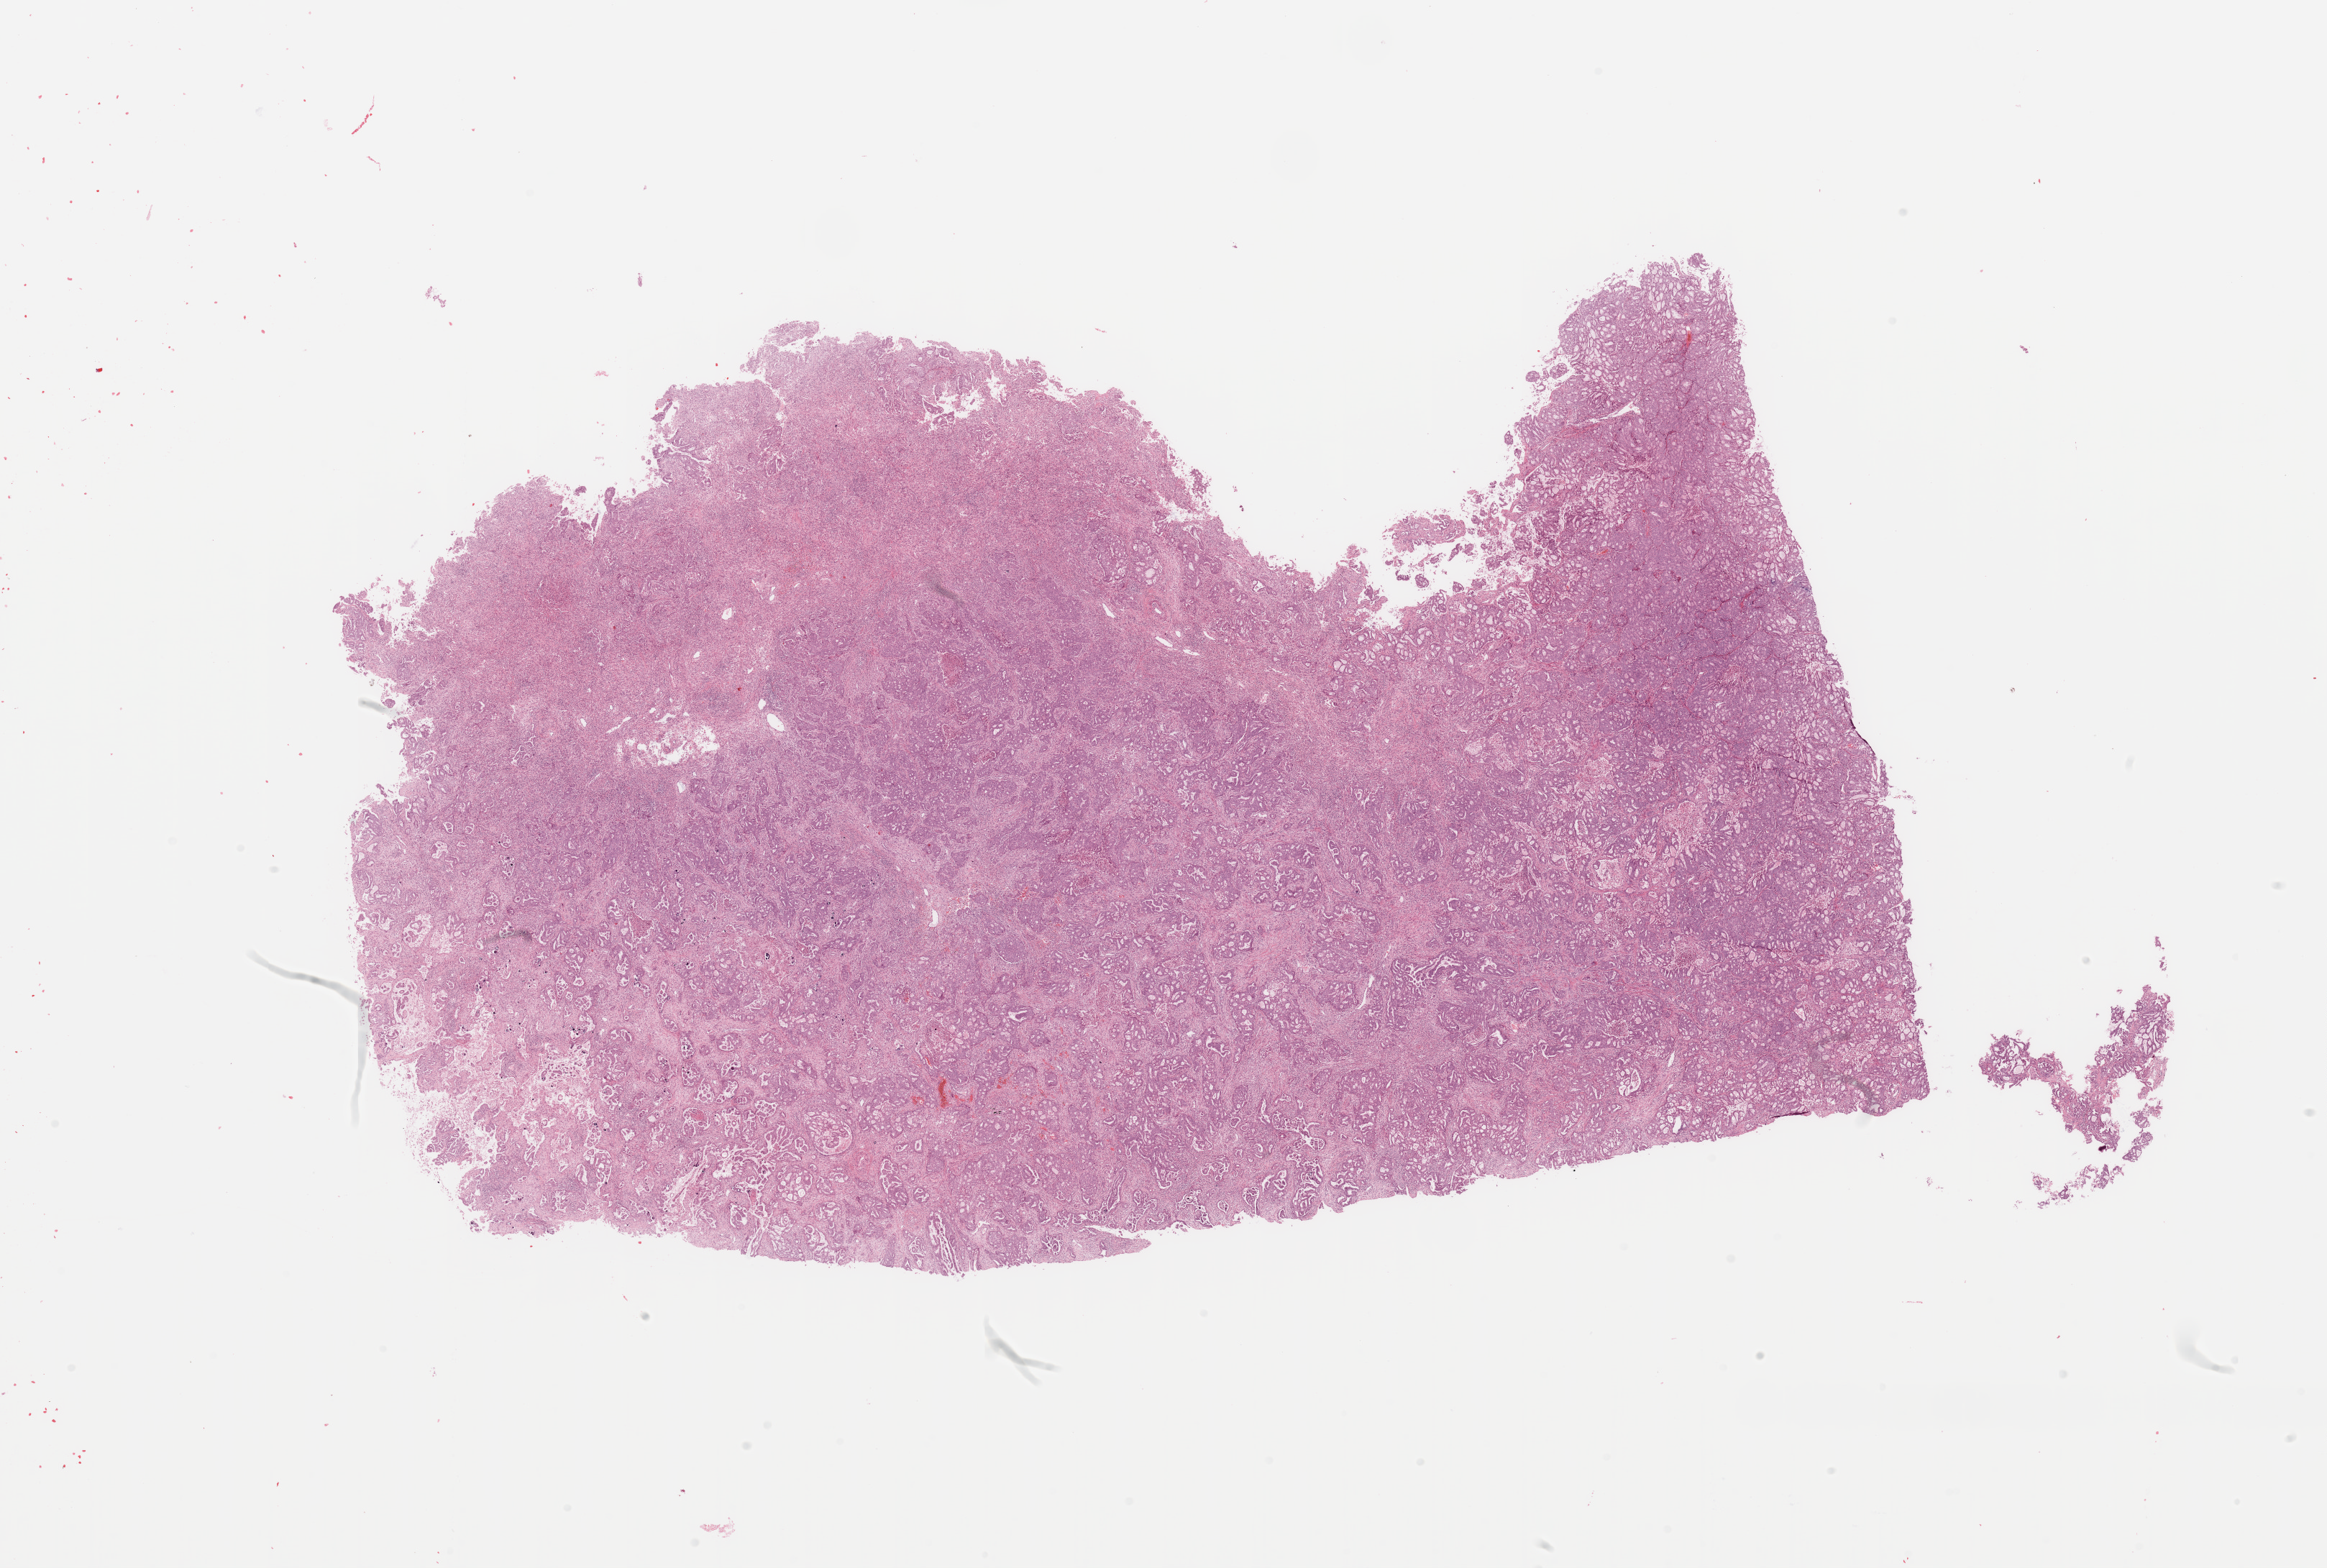
Whole-slide histology image, Hematoxylin and eosin (H&E) stained — a low-resolution overview of the entire scanned area, about 25.6 x 17.3 mm. Lung, tumour tissue. Male, 58 y/o. Histologic grade: G2 (moderately differentiated).
• diagnosis: Adenocarcinoma, NOS
• primary tumour site (as recorded): left lower lobe
• AJCC pathologic stage: IB